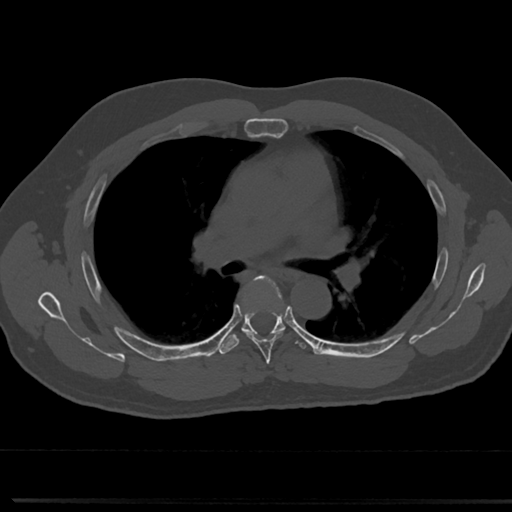
CT including the spine, one axial slice. Position 478 of 817 along the scan axis. Reconstruction kernel Br40s/3. 120 kVp. Bone window (W 1800 / L 400 HU). 0.5 mm slice thickness. 512 × 512 image matrix, field of view 355 × 355 mm. Patient: male, 61 years. Case-level facts recorded for this patient, not image findings: primary cancer: prostate.
Annotated regions visible in this slice (semi-automatic segmentation, software-assisted and operator-edited):
- T5 vertebra: box from (x=238, y=277) to (x=288, y=359) px
- T6 vertebra: (x=240, y=324)–(x=287, y=335)